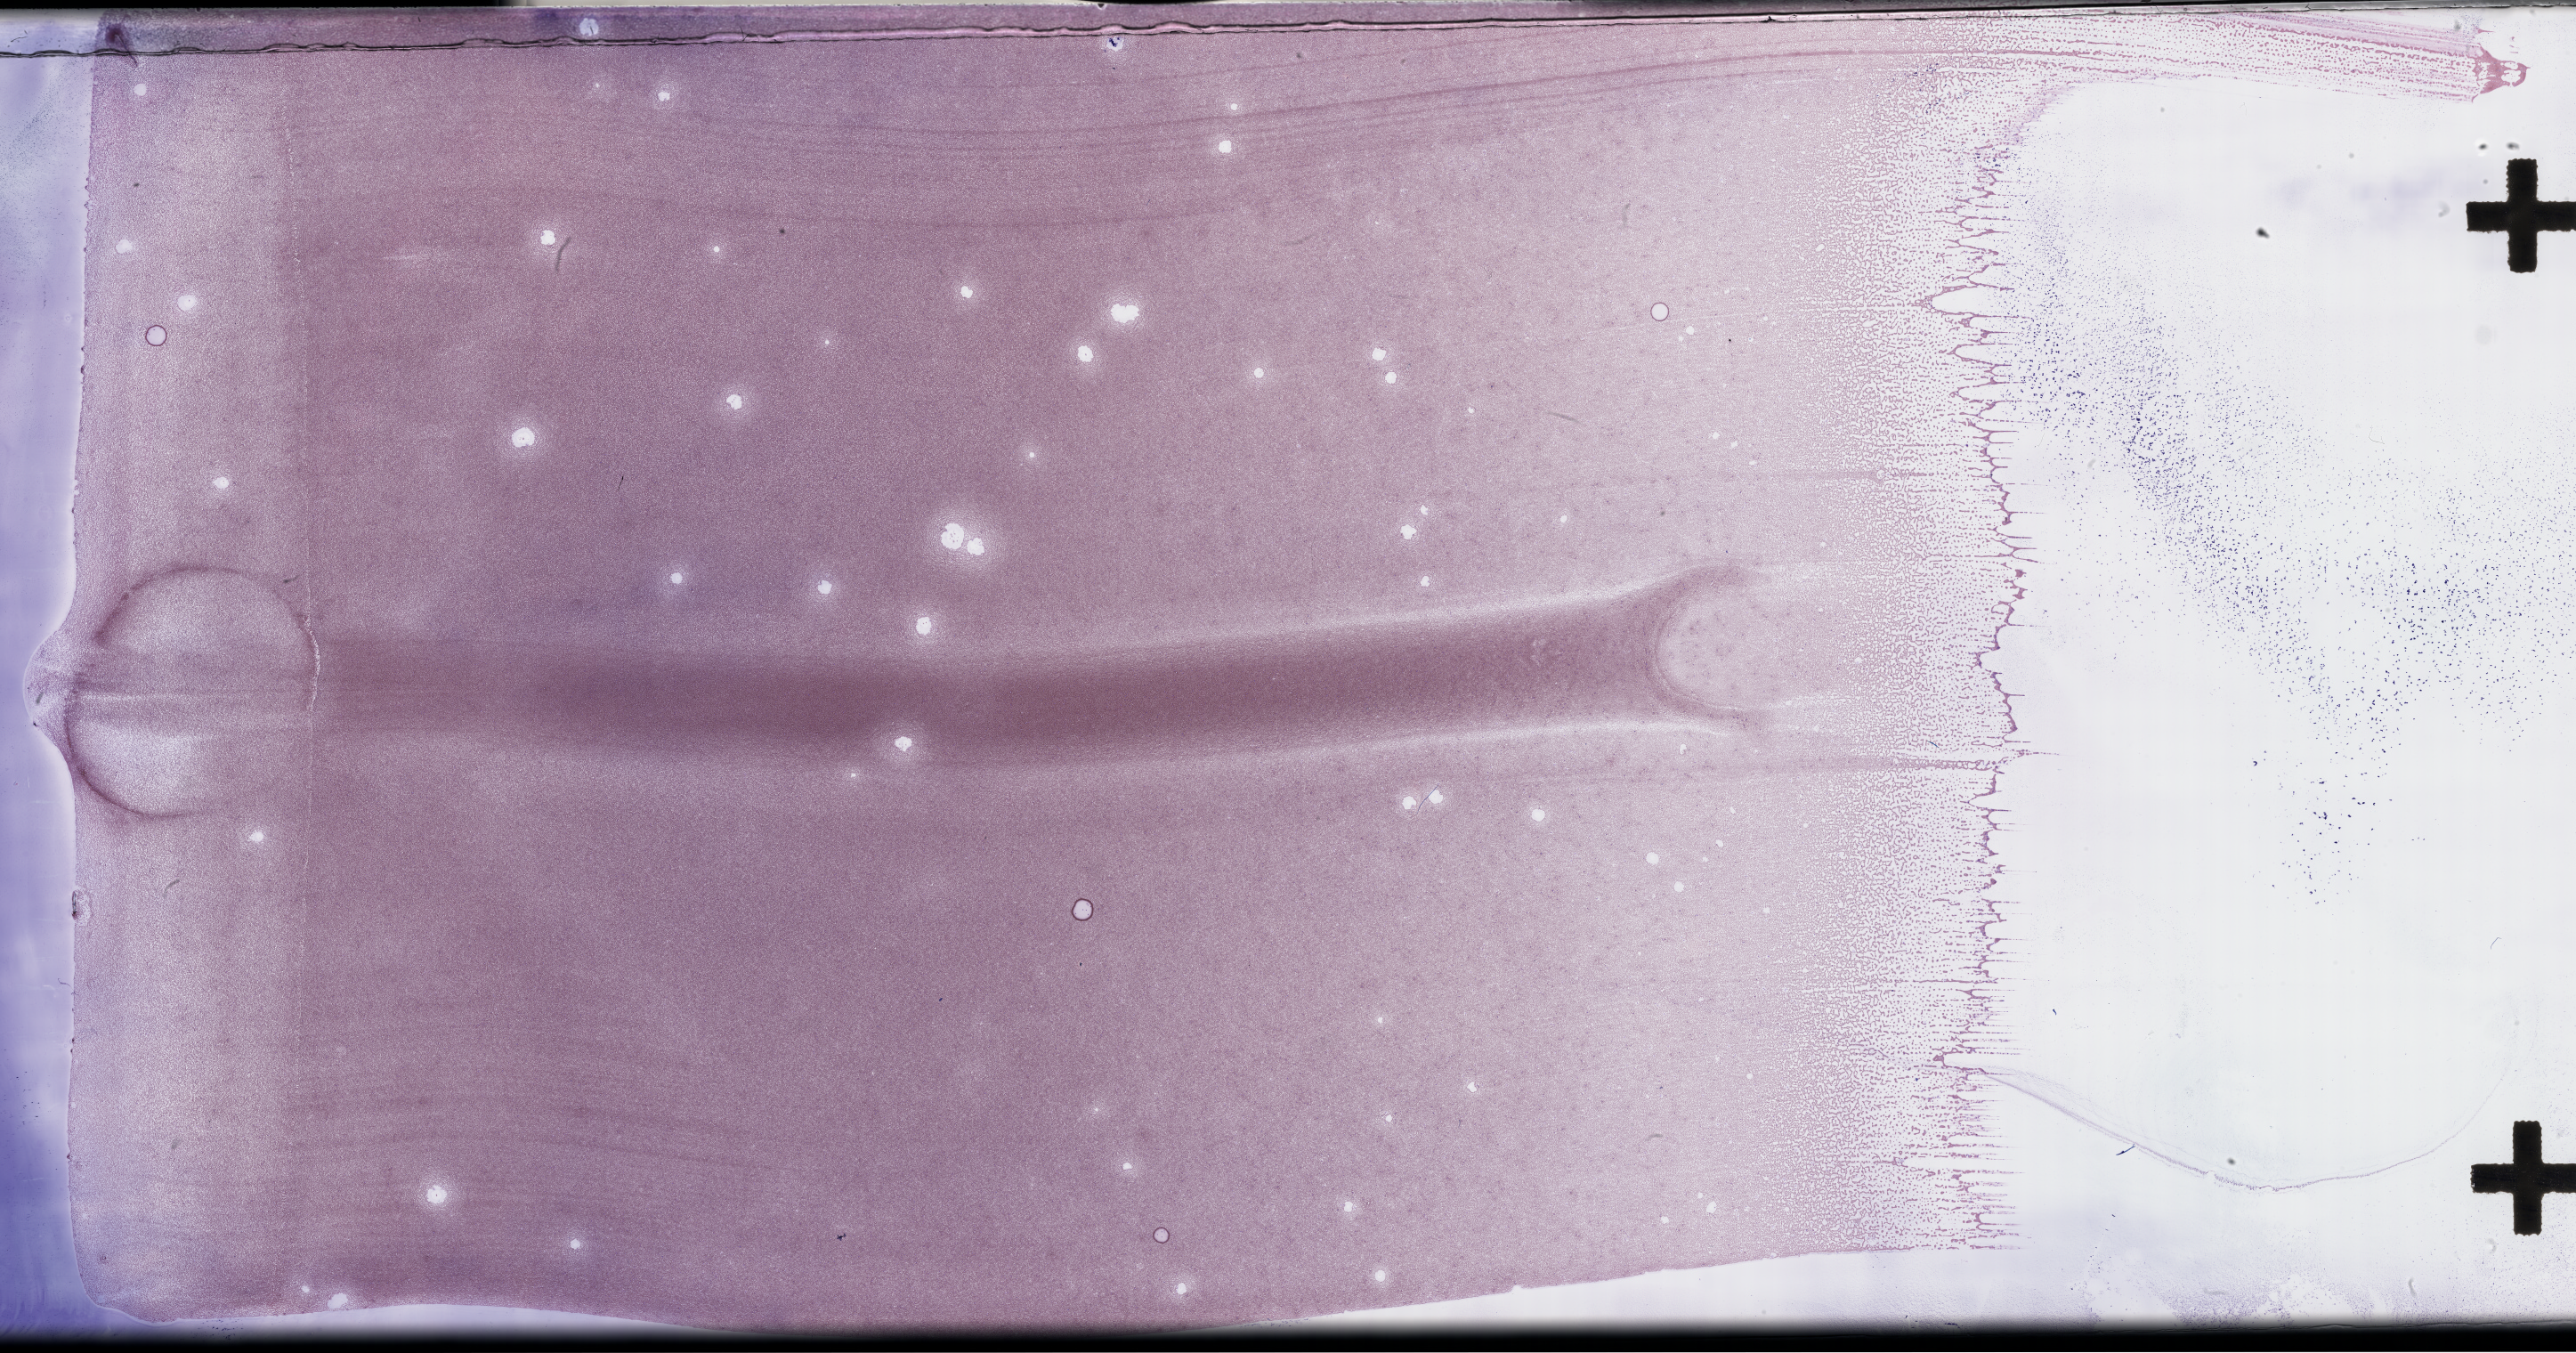
Whole-slide image of a bone marrow smear, Wright-Giemsa stain — a low-resolution overview of the entire scanned area, about 46.7 x 24.5 mm; smear from an EDTA sample. Male patient.
From a patient with: Plasma Cell Myeloma.